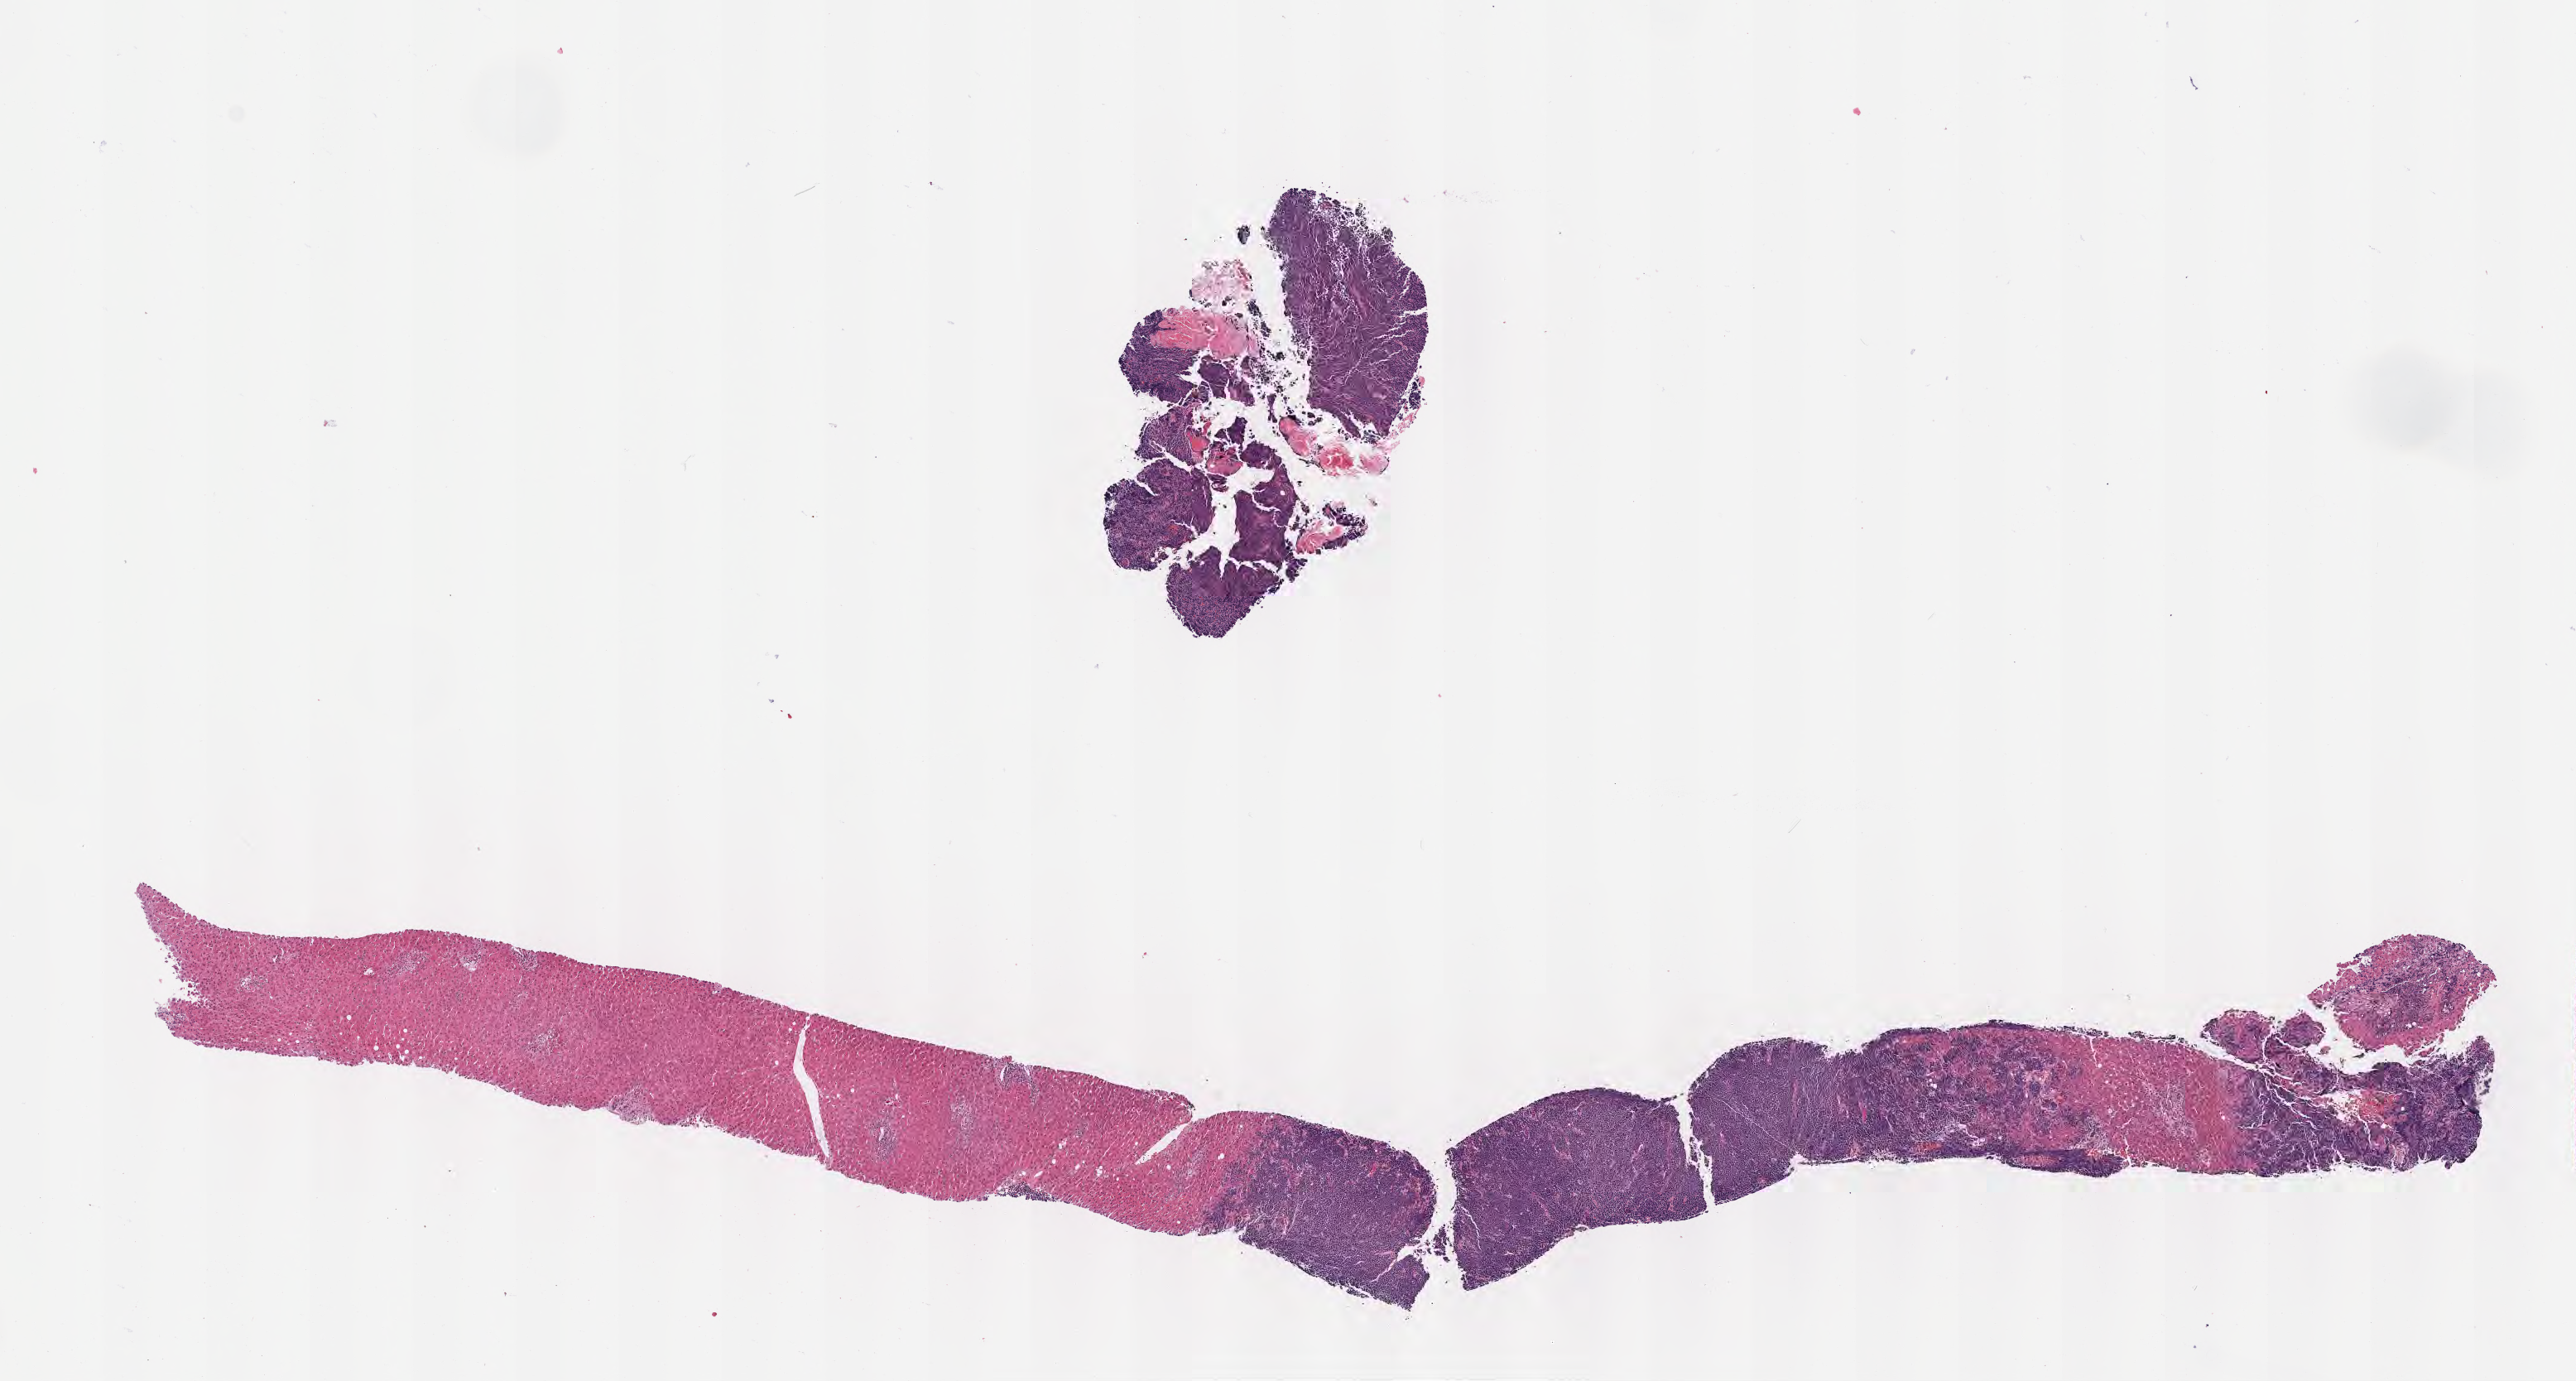
Whole-slide image, hematoxylin and eosin (H&E) stain, shown as a low-resolution overview of the whole scanned area (about 12.6 x 6.7 mm). Tumor tissue. Male patient, age 68 years.
Diagnosis: Burkitt lymphoma, NOS.